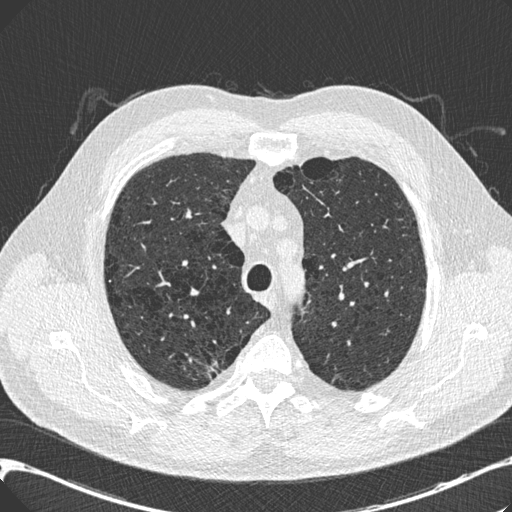
Chest CT (low-dose screening protocol), one axial image; third annual screen; lung window (W 1500 / L -600 HU); 0.75 mm slice thickness; slice 45 of 197 in the series; 512 × 512 image matrix. Male, age 68 years at enrolment.
- Expert reader's lesion annotation, box from (x=189, y=349) to (x=235, y=393) px.
- The screening reader recorded 3 non-calcified nodules or masses ≥4 mm on this exam (right upper lobe, right upper lobe, left lower lobe); which of them this box marks is not recorded.
- Official screen result: positive, other.
- Later outcome: lung cancer diagnosed 46 days after this screen — adenocarcinoma, NOS, right upper lobe, well differentiated (G1), stage IB (AJCC 6th edition), 15 mm at pathology.